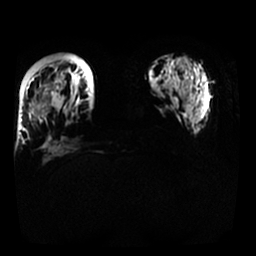
Breast MRI, one axial slice. Diffusion-weighted series; image 2 of 4 stored at this slice position (different b-values; order by instance number). 1.5 T. 256 × 256 image matrix, field of view 340 × 340 mm. Female patient.
Outlined on this slice (outlined manually by an expert reader):
- tumour on diffusion-weighted imaging: box from (x=40, y=106) to (x=50, y=114) px